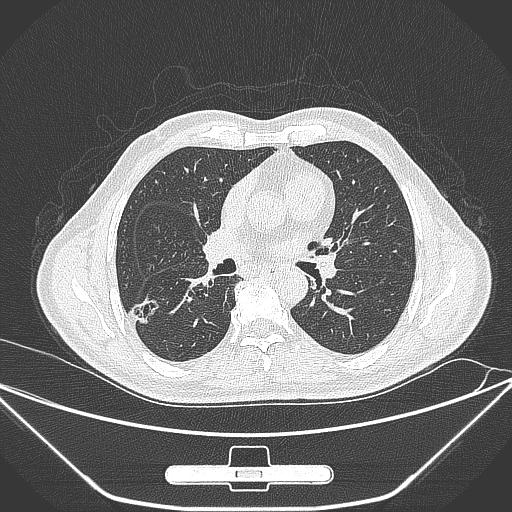
Chest CT, one axial slice; position 152 of 309 along the scan axis; lung window (W 1500 / L -600 HU); 1 mm slice thickness; 512 × 512 image matrix, field of view 398 × 398 mm. Male patient, age 71 years. Case-level facts recorded for this patient, not image findings: clinical TNM (as recorded): T1c N0 M0; histopathological grade: G2.
Outlined on this slice (rectangle marked by the reading radiologist):
- lung tumour (recorded histology: adenocarcinoma): bounding box [x1, y1, x2, y2] px = [125, 292, 164, 327]